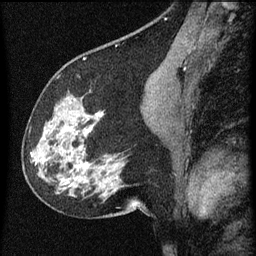
Breast MRI (dynamic contrast-enhanced), one sagittal slice. Position 32 of 60 along the scan axis. Dynamic contrast-enhanced series, image 2 of 3 at this slice position (ordered by acquisition). 1.5 T. TE 4.2 ms, TR 8 ms. 2 mm slice thickness. 256 × 256 image matrix. Female patient, age 61 years.
Outlined on this slice (semi-automatically segmented with operator editing):
- analysis volume of interest (the breast-tissue region the enhancement analysis was run in; not a lesion): box from (x=27, y=80) to (x=139, y=209) px
- tumour enhancement mask (voxels above the 70 % enhancement threshold inside the analysis volume of interest): (x=30, y=114)–(x=98, y=165)